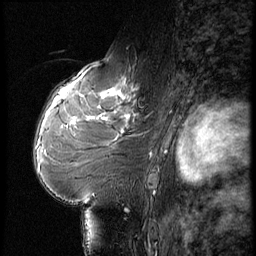
Breast MRI (dynamic contrast-enhanced), one sagittal slice. Dynamic contrast-enhanced series, image 2 of 3 at this slice position (ordered by acquisition). 1.5 T. TE 4.2 ms, TR 9 ms. 256 × 256 image matrix, field of view 180 × 180 mm. Female patient, age 61 years. From the clinical record (not read from this slice): setting: breast cancer imaged before/during neoadjuvant chemotherapy; receptor status: HR-positive, HER2-negative.
Structures marked on this image (semi-automatically segmented with operator editing):
- analysis volume of interest (the breast-tissue region the enhancement analysis was run in; not a lesion): bounding box [x1, y1, x2, y2] px = [65, 74, 149, 175]
- tumour enhancement mask (voxels above the 140 % enhancement threshold inside the analysis volume of interest): [68, 89, 126, 127]